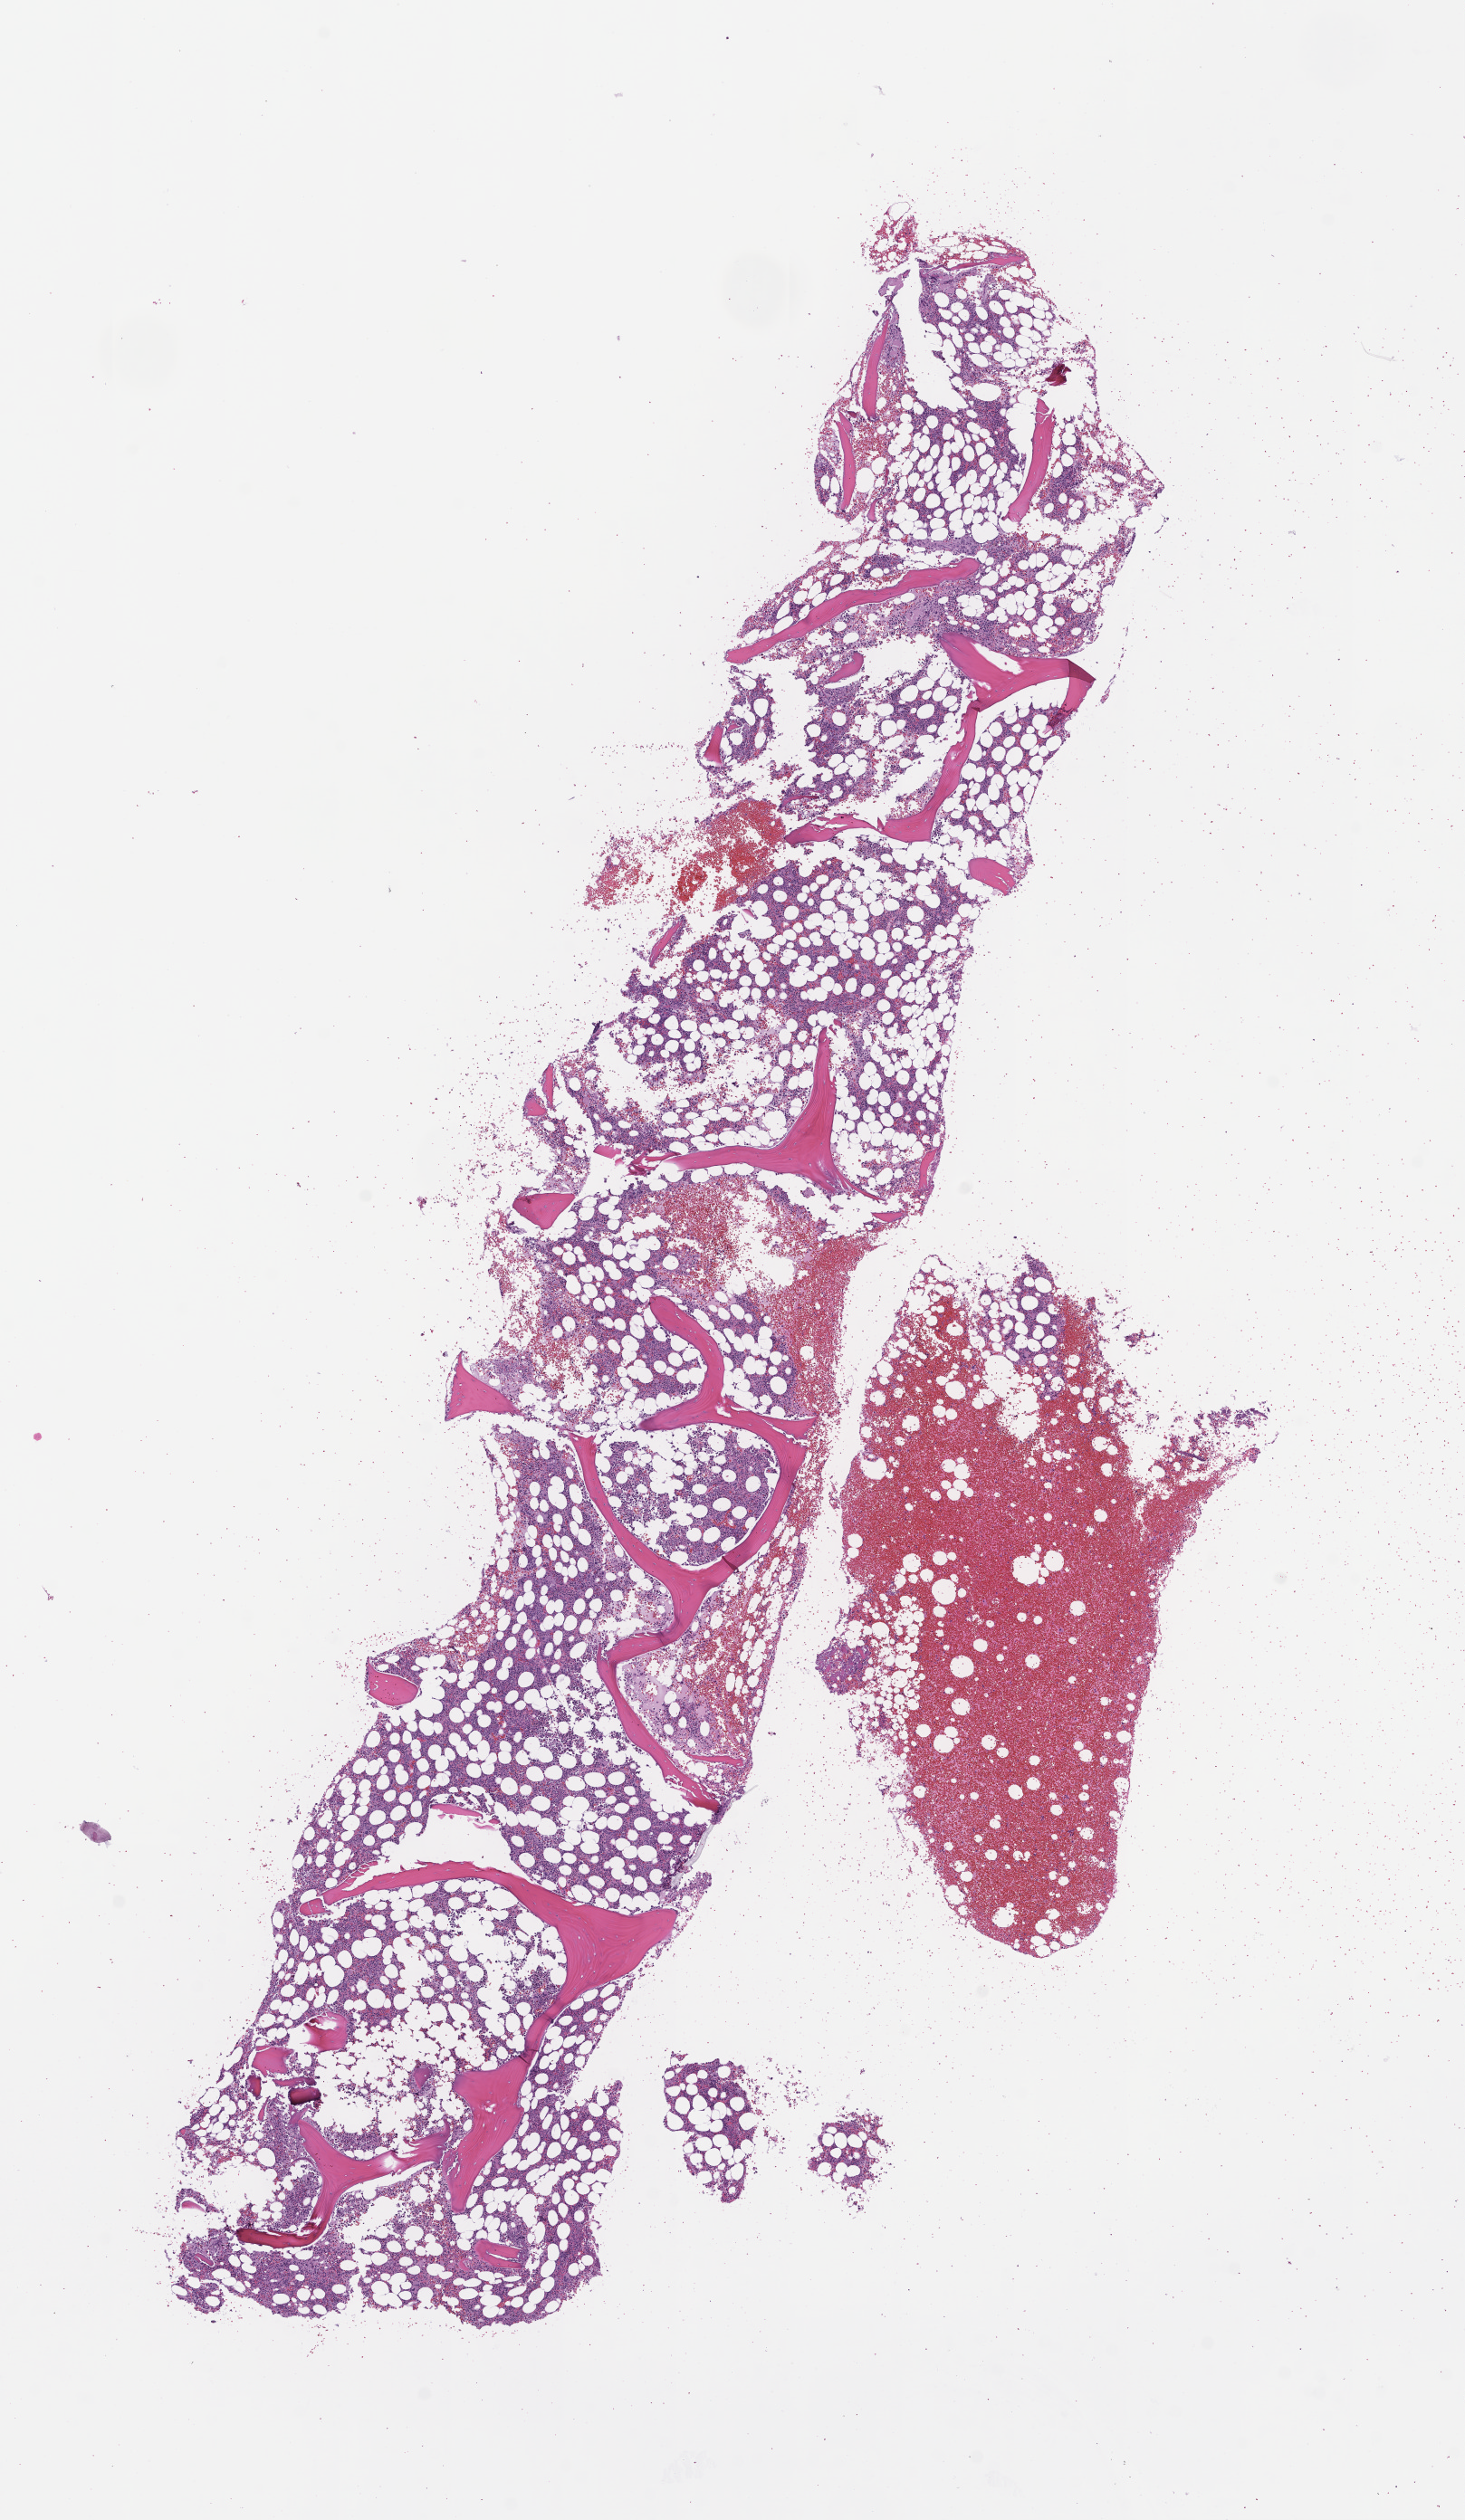
Digitized hematoxylin and eosin (H&E)-stained section, low-resolution overview of the scanned area, about 6.5 x 11.2 mm; formalin-fixed paraffin-embedded section; tissue site: bone marrow; archival tissue. Patient sex: male.
This section: primary tumor. Diagnosis: Plasma Cell Myeloma.